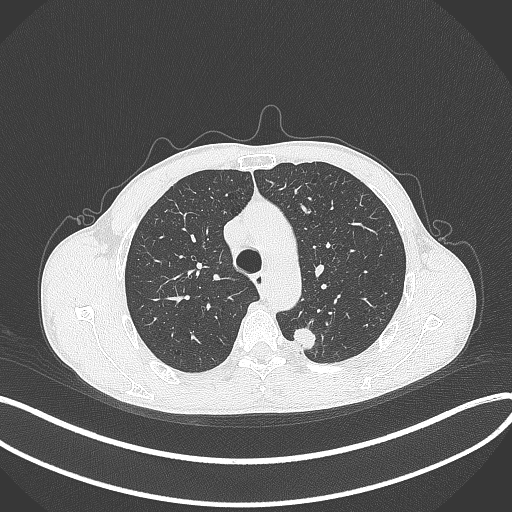
Chest CT, one axial slice; slice 291 of 429 in the series (ordered by position); reconstruction kernel B70f; 120 kVp; lung window (W 1500 / L -600 HU); 1 mm slice thickness; 512 × 512 image matrix, field of view 400 × 400 mm. Male patient, age 51 years. Case-level facts recorded for this patient, not image findings: clinical TNM (as recorded): T2a N1 M1.
Annotated regions visible in this slice (rectangle marked by the reading radiologist):
- lung tumour (recorded histology: adenocarcinoma): bounding box (x1, y1, x2, y2) in pixels: (288, 327, 319, 351)